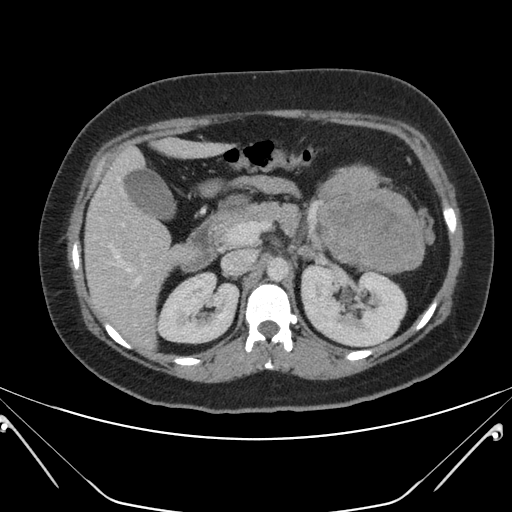
Contrast-enhanced abdominal CT, one axial slice; position 123 of 168 along the scan axis; 120 kVp; intravenous contrast given; soft-tissue window (W 400 / L 40 HU); 512 × 512 image matrix, field of view 394 × 394 mm. Female patient, age 26 years. Case-level facts recorded for this patient, not image findings: diagnosis: adrenocortical carcinoma; tumour side: left adrenal; tumour size at pathology: 28 cm; Ki-67 index: 20 %; stage (as recorded): 2.
Annotated regions visible in this slice (semi-automatic segmentation, software-assisted and operator-edited):
- mass: bounding box (x1, y1, x2, y2) in pixels: (321, 169, 422, 270)